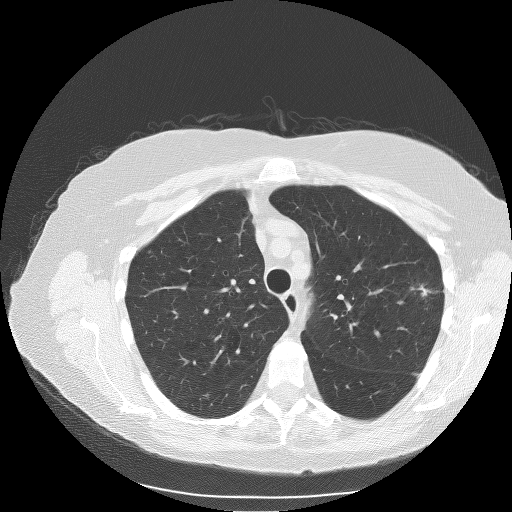
Chest CT (low-dose screening protocol), one axial image. First (baseline) screen. Lung window (W 1500 / L -600 HU). Slice 71 of 106 in the series. Female, age 71 years at enrolment.
Expert-annotated lung lesion, bounding box [x1, y1, x2, y2] px = [405, 280, 438, 312]. Reader record for this screening exam (exam-level; its link to the box is not recorded): non-calcified nodule or mass ≥4 mm, left upper lobe, 15 × 9 mm, spiculated (stellate) margins, soft tissue attenuation. Participant outcome: lung cancer diagnosed 77 days after this screen — adenocarcinoma, NOS, left upper lobe, moderately differentiated (G2), stage IA (AJCC 6th edition), 15 mm at pathology.